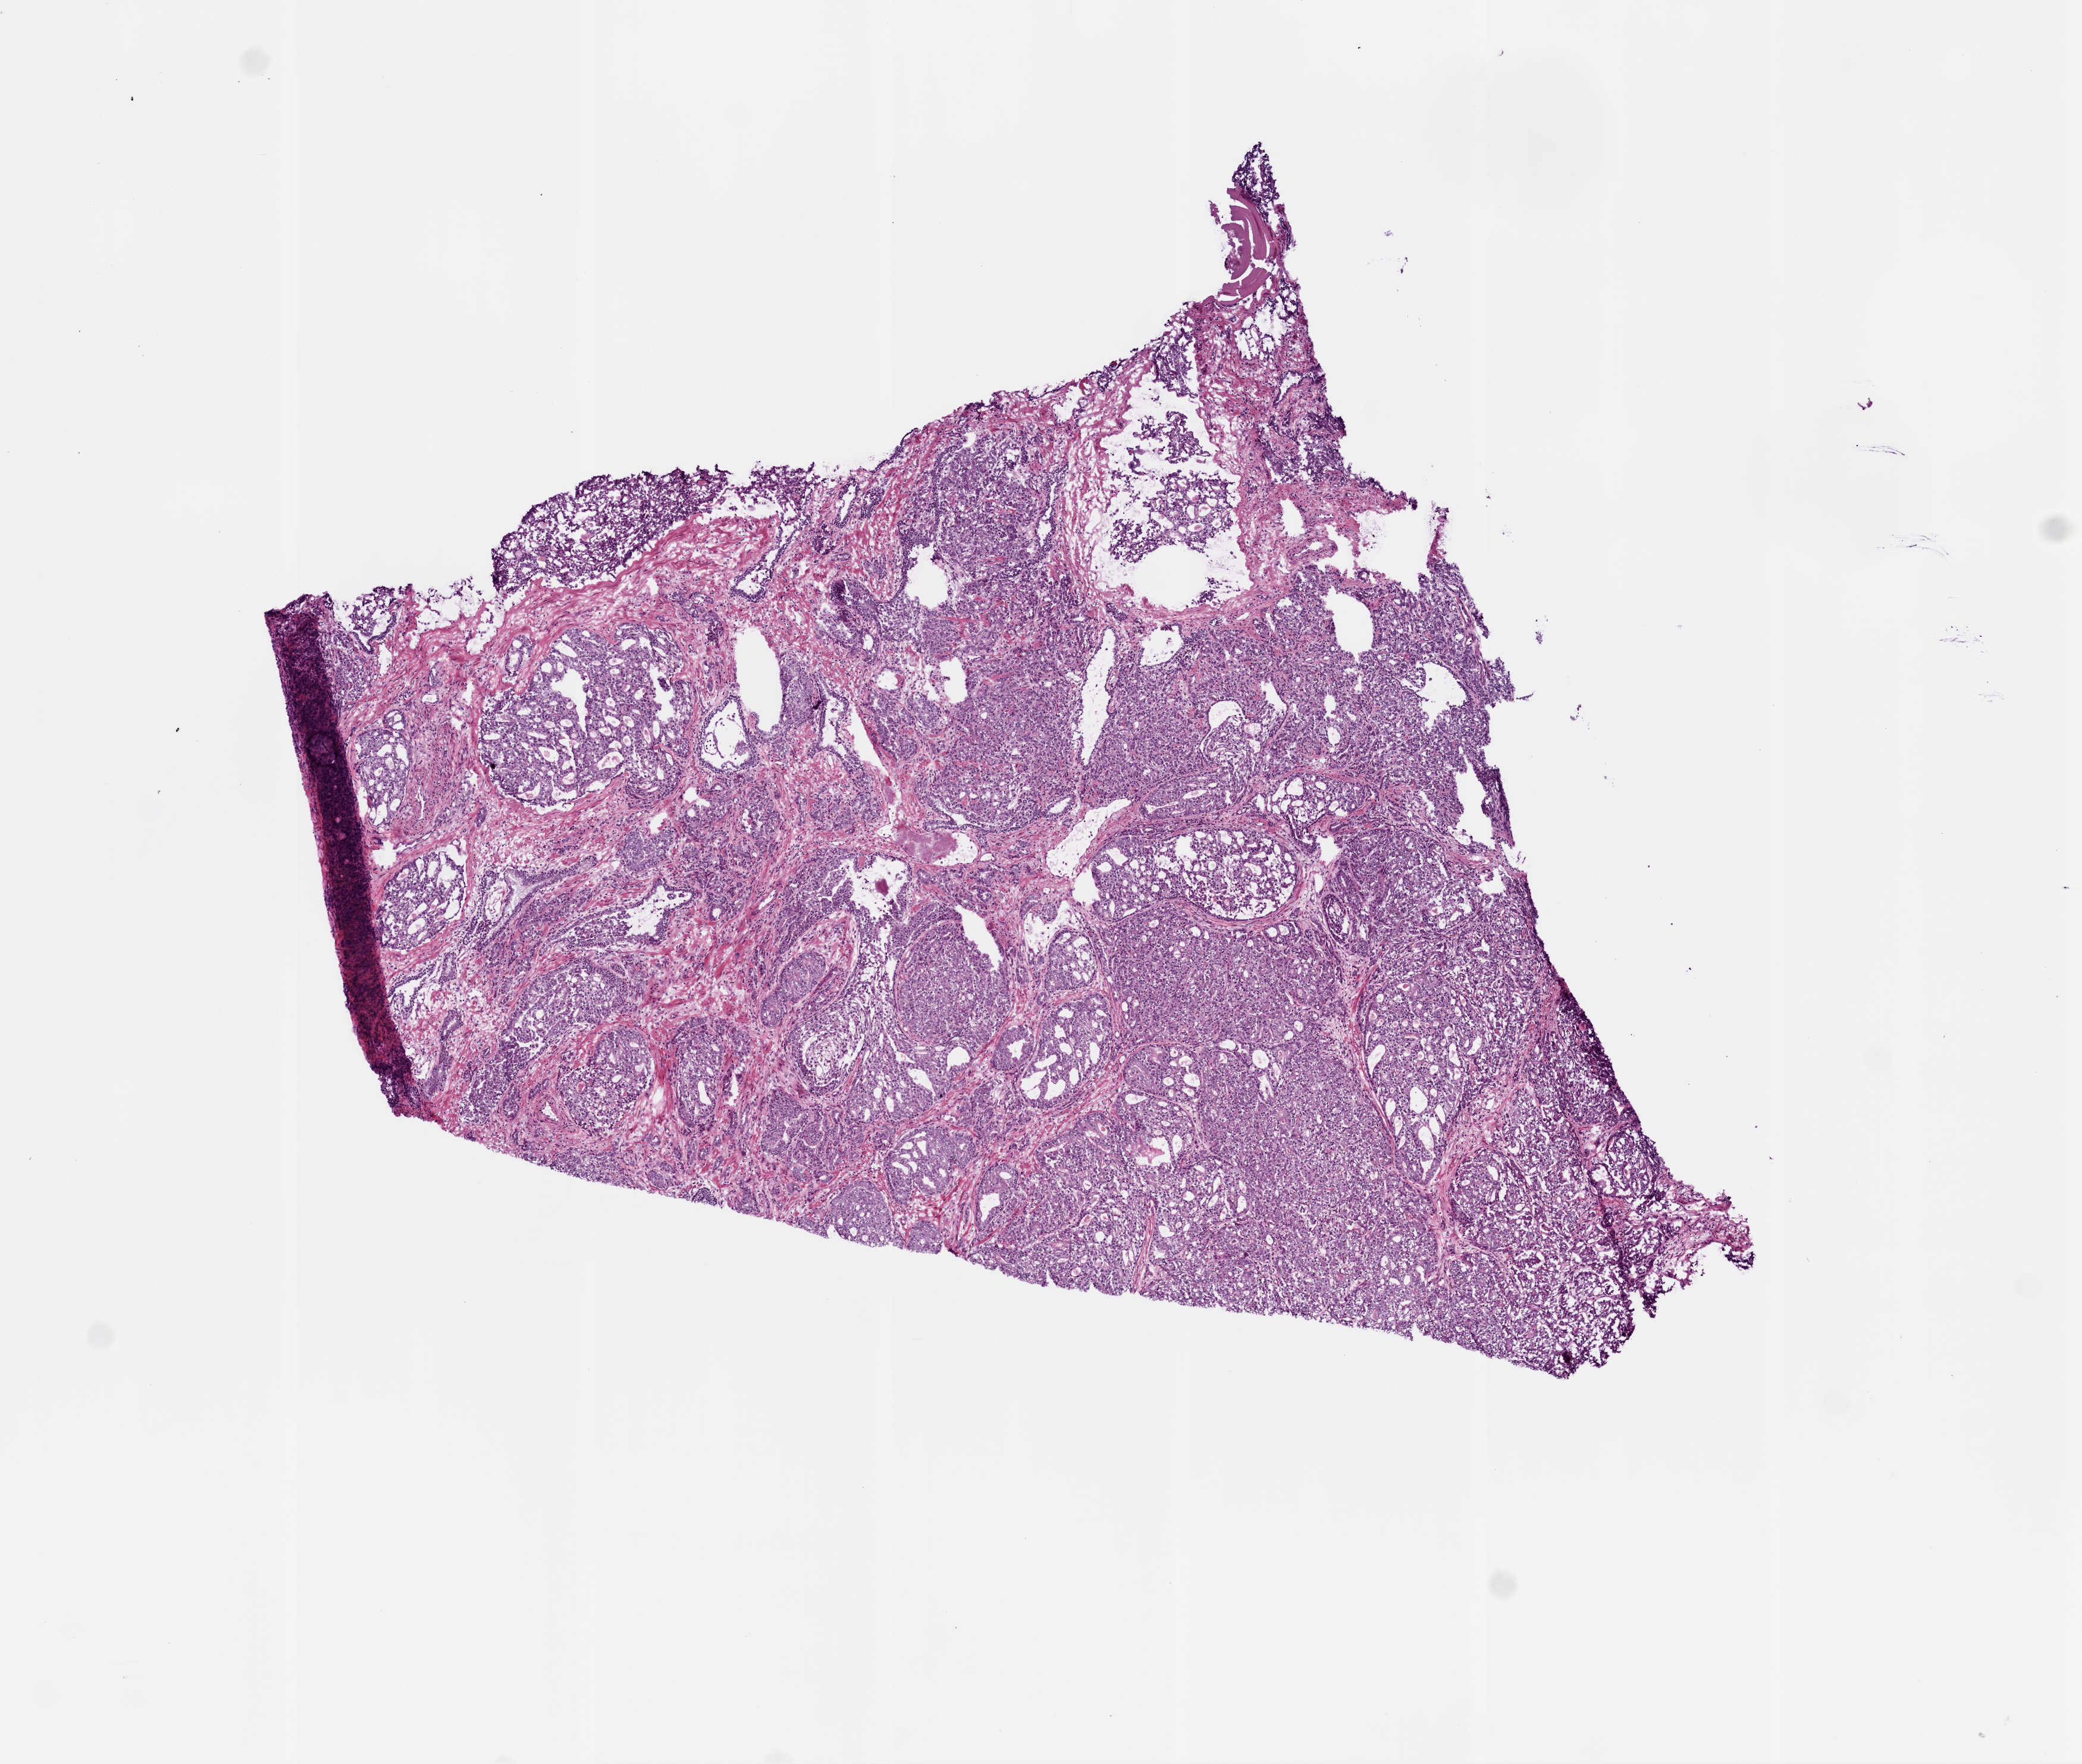
Whole-slide histology image, Hematoxylin and eosin (H&E) stained, shown as a low-resolution overview of the whole scanned area (about 7.0 x 5.9 mm, from a 20x scan); frozen section from the bottom of the tissue portion; prostate, primary tumour sample. Male patient; age at initial diagnosis 56 years. Gleason score: 9 (4+5). Composition of this section per pathologist review: tumour cells 90%, tumour nuclei 90%, normal cells 4%, stromal cells 6%, necrosis 0%. Inflammatory infiltration, as recorded: lymphocyte infiltration 0%, monocyte infiltration 0%, neutrophil infiltration 0%.
* diagnosis: Acinar cell carcinoma (prostate gland)
* laterality: bilateral
* lymph nodes positive (case pathology): 1 of 5 examined